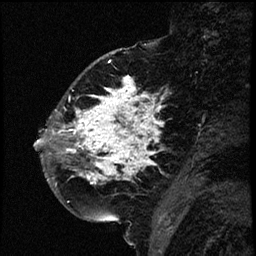
Breast MRI (dynamic contrast-enhanced), one sagittal slice. Slice 23 of 66 in the series (ordered by position). Dynamic contrast-enhanced study with each time point stored as its own series, time point 2 of 3 at this slice position (early post-contrast, ordered by acquisition time). 1.5 T. TE 4.2 ms, TR 17.6 ms. 2 mm slice thickness. 256 × 256 image matrix, field of view 200 × 200 mm. Female patient. Case-level facts recorded for this patient, not image findings: setting: breast cancer imaged before/during neoadjuvant chemotherapy; receptor status: HER2-positive.
Outlined on this slice (semi-automatically segmented with operator editing):
- analysis volume of interest (the breast-tissue region the enhancement analysis was run in; not a lesion): bounding box [x1, y1, x2, y2] px = [52, 69, 177, 209]
- tumour enhancement mask (voxels above the 100 % enhancement threshold inside the analysis volume of interest): [52, 76, 161, 185]